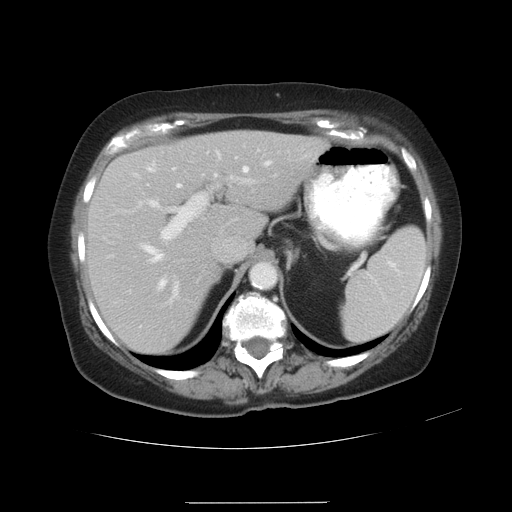
Contrast-enhanced abdominal CT, one axial slice. Slice 21 of 32 in the series (ordered by position). Reconstruction kernel STANDARD. Soft-tissue window (W 400 / L 40 HU). 7.5 mm slice thickness. 512 × 512 image matrix, field of view 386 × 386 mm. Female patient, age 65 years. Case-level facts recorded for this patient, not image findings: diagnosis: colorectal cancer liver metastases, imaged before liver resection; multiple liver metastases: yes; largest metastasis: 1.7 cm; disease in both lobes: no.
Outlined on this slice (outlined manually by an expert reader):
- hepatic veins: bounding box <147,166,249,304> (left, top, right, bottom; pixels)
- liver: <89,132,324,350>
- planned liver remnant (the part of the liver to remain after resection): <89,136,236,350>
- portal vein (with intrahepatic branches): <139,156,255,261>